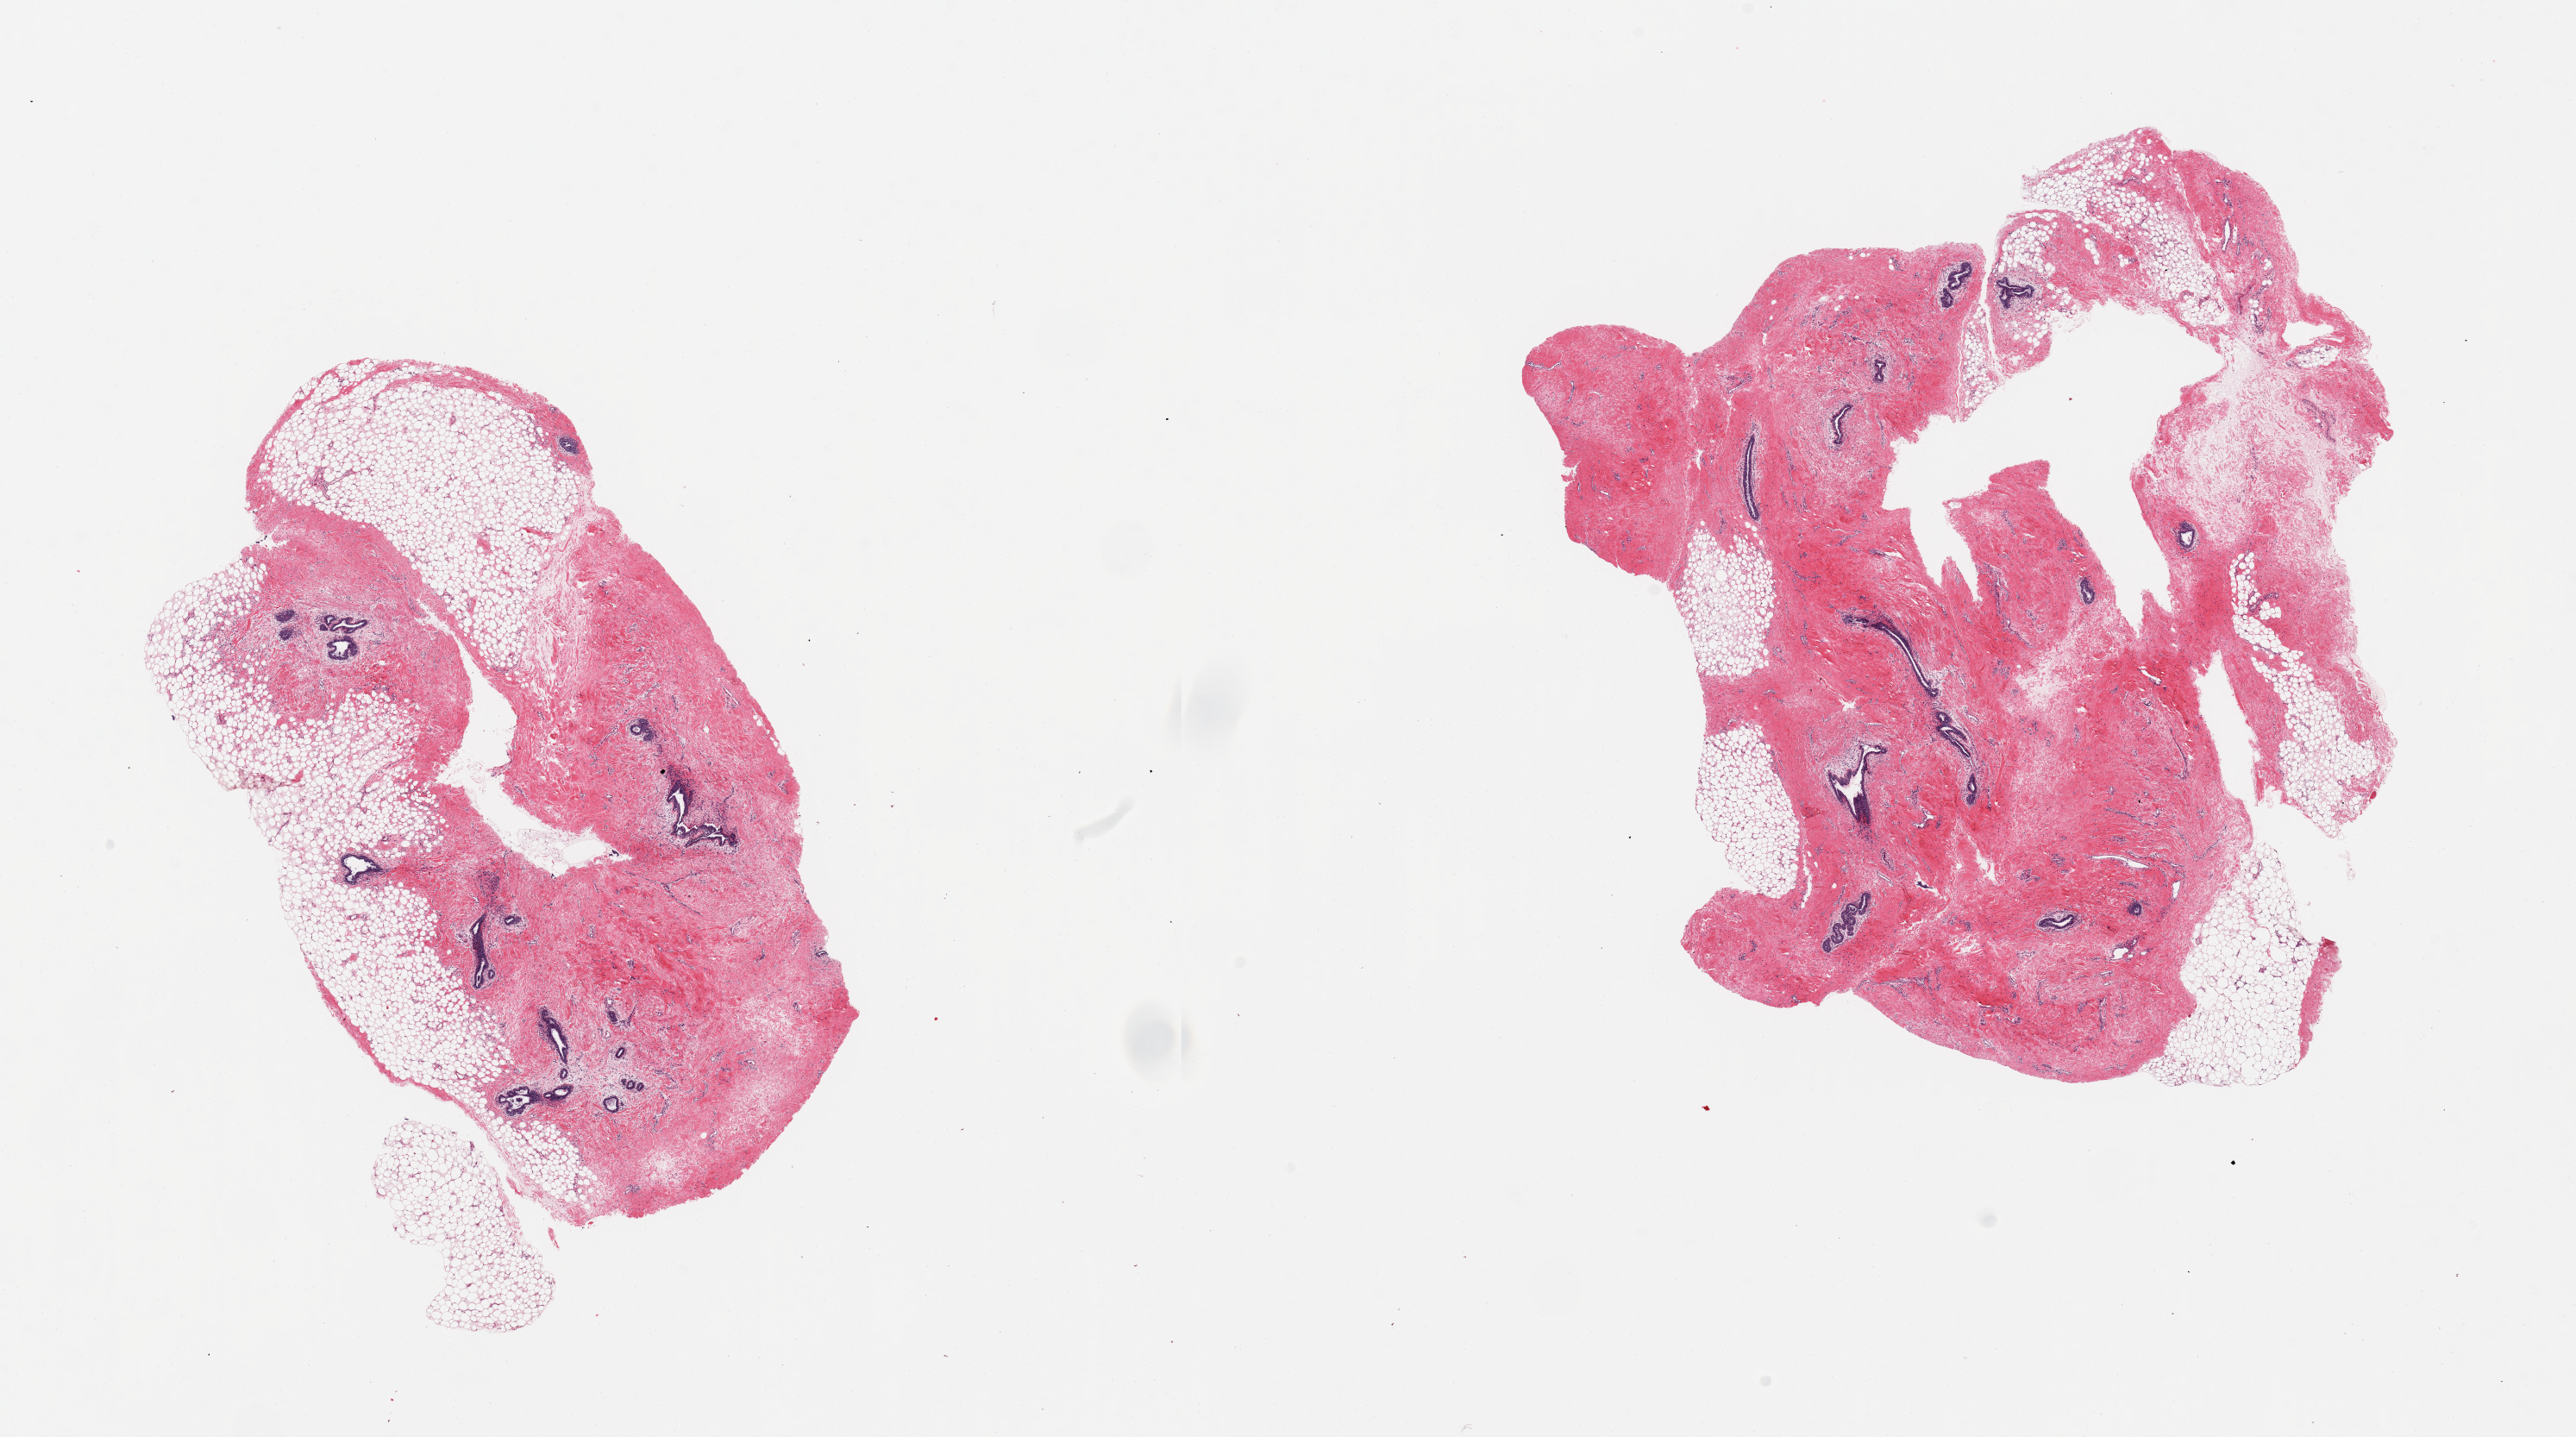
Whole-slide image, hematoxylin and eosin (H&E) stain, brightfield, shown as a low-resolution overview of the whole scanned area (about 23.6 x 13.2 mm), PAXgene-fixed, paraffin-embedded tissue, sampled site (target tissue): breast, tissue donor sample.
Reviewer comment on this tissue sample: 2 pieces; ductal proliferation and fibrosis consistent with liver cirrhosis.